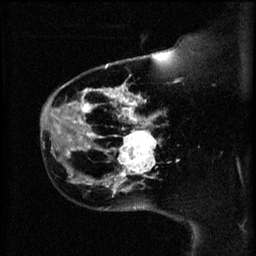
Breast MRI (dynamic contrast-enhanced), one sagittal slice. Slice 45 of 60 in the series (ordered by position). 3 images stored at this slice position (order not interpretable as contrast timing). 1.5 T. TE 4.2 ms, TR 11 ms. 2 mm slice thickness. 256 × 256 image matrix, field of view 180 × 180 mm. Female patient, age 44 years.
Annotated regions visible in this slice (semi-automatic segmentation, software-assisted and operator-edited):
- analysis volume of interest (the breast-tissue region the enhancement analysis was run in; not a lesion): bounding box (x1, y1, x2, y2) in pixels: (110, 124, 163, 179)
- tumour enhancement mask (voxels above the 70 % enhancement threshold inside the analysis volume of interest): (116, 124, 157, 179)